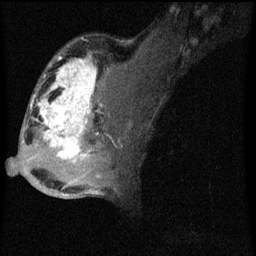
Breast MRI (dynamic contrast-enhanced), one sagittal slice. Position 34 of 60 along the scan axis. Dynamic contrast-enhanced series, image 2 of 4 at this slice position (ordered by acquisition). 1.5 T. TE 4.2 ms, TR 8 ms. 256 × 256 image matrix. Patient: female, 50 years.
Outlined on this slice (semi-automatically segmented with operator editing):
- analysis volume of interest (the breast-tissue region the enhancement analysis was run in; not a lesion): bounding box (x1, y1, x2, y2) in pixels: (26, 44, 124, 177)
- tumour enhancement mask (voxels above the 70 % enhancement threshold inside the analysis volume of interest): (32, 56, 103, 163)